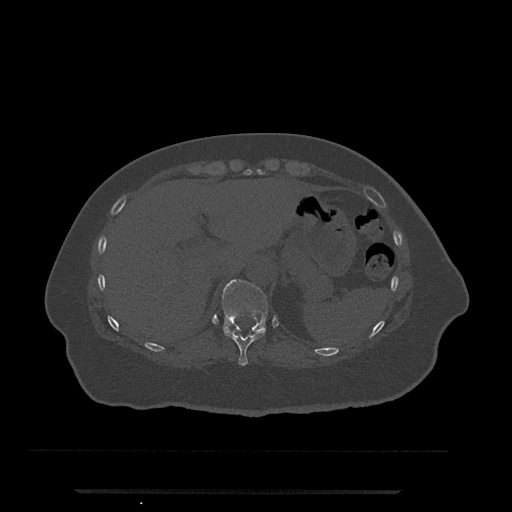
CT including the spine, one axial slice; slice 257 of 797 in the series (ordered by position); reconstruction kernel Br40s/3; 120 kVp; bone window (W 1800 / L 400 HU); 512 × 512 image matrix, field of view 440 × 440 mm. Female patient, age 51 years. Case-level facts recorded for this patient, not image findings: primary cancer: neuro; vertebrae with lytic lesions (as recorded): T8.
Outlined on this slice (semi-automatic segmentation, software-assisted and operator-edited):
- T10 vertebra: box from (x=223, y=328) to (x=266, y=366) px
- T11 vertebra: (x=222, y=279)–(x=276, y=334)